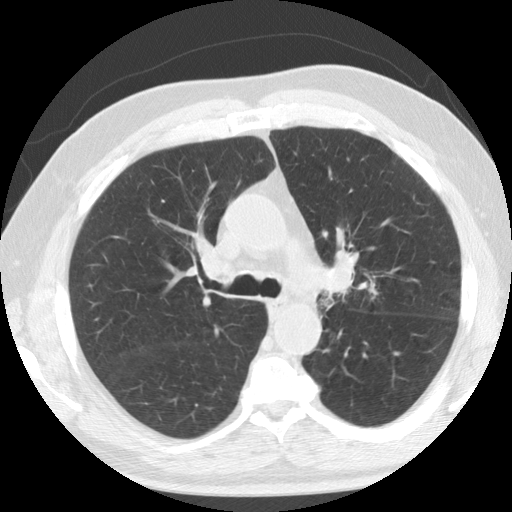
Low-dose screening chest CT, one axial slice. Slice 87 of 133 in the series (ordered by position). Reconstruction kernel STANDARD. Lung window (W 1500 / L -600 HU). 2.5 mm slice thickness. 512 × 512 image matrix, field of view 342 × 342 mm.
Outlined on this slice (expert manual segmentation):
- lesion 1 (tumor, upper lobe of left lung): bounding box [x1, y1, x2, y2] px = [323, 252, 355, 293]